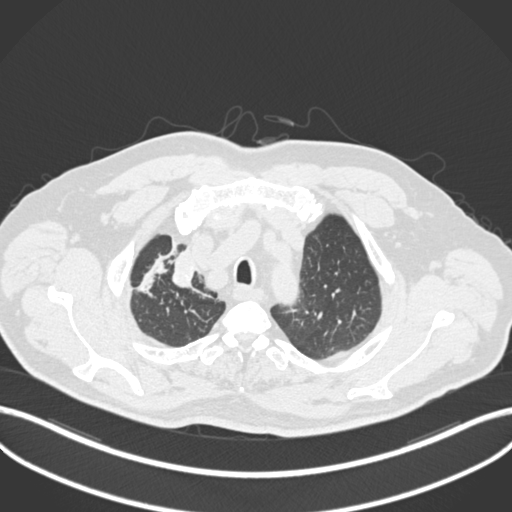
Chest CT, one axial slice; 120 kVp; lung window (W 1500 / L -600 HU); 512 × 512 image matrix, field of view 400 × 400 mm. Patient: male, 60 years. From the clinical record (not read from this slice): clinical TNM (as recorded): T1b N1 M0.
Outlined on this slice (bounding box drawn by a radiologist):
- lung tumour (recorded histology: squamous cell carcinoma): bounding box <167,240,204,293> (left, top, right, bottom; pixels)